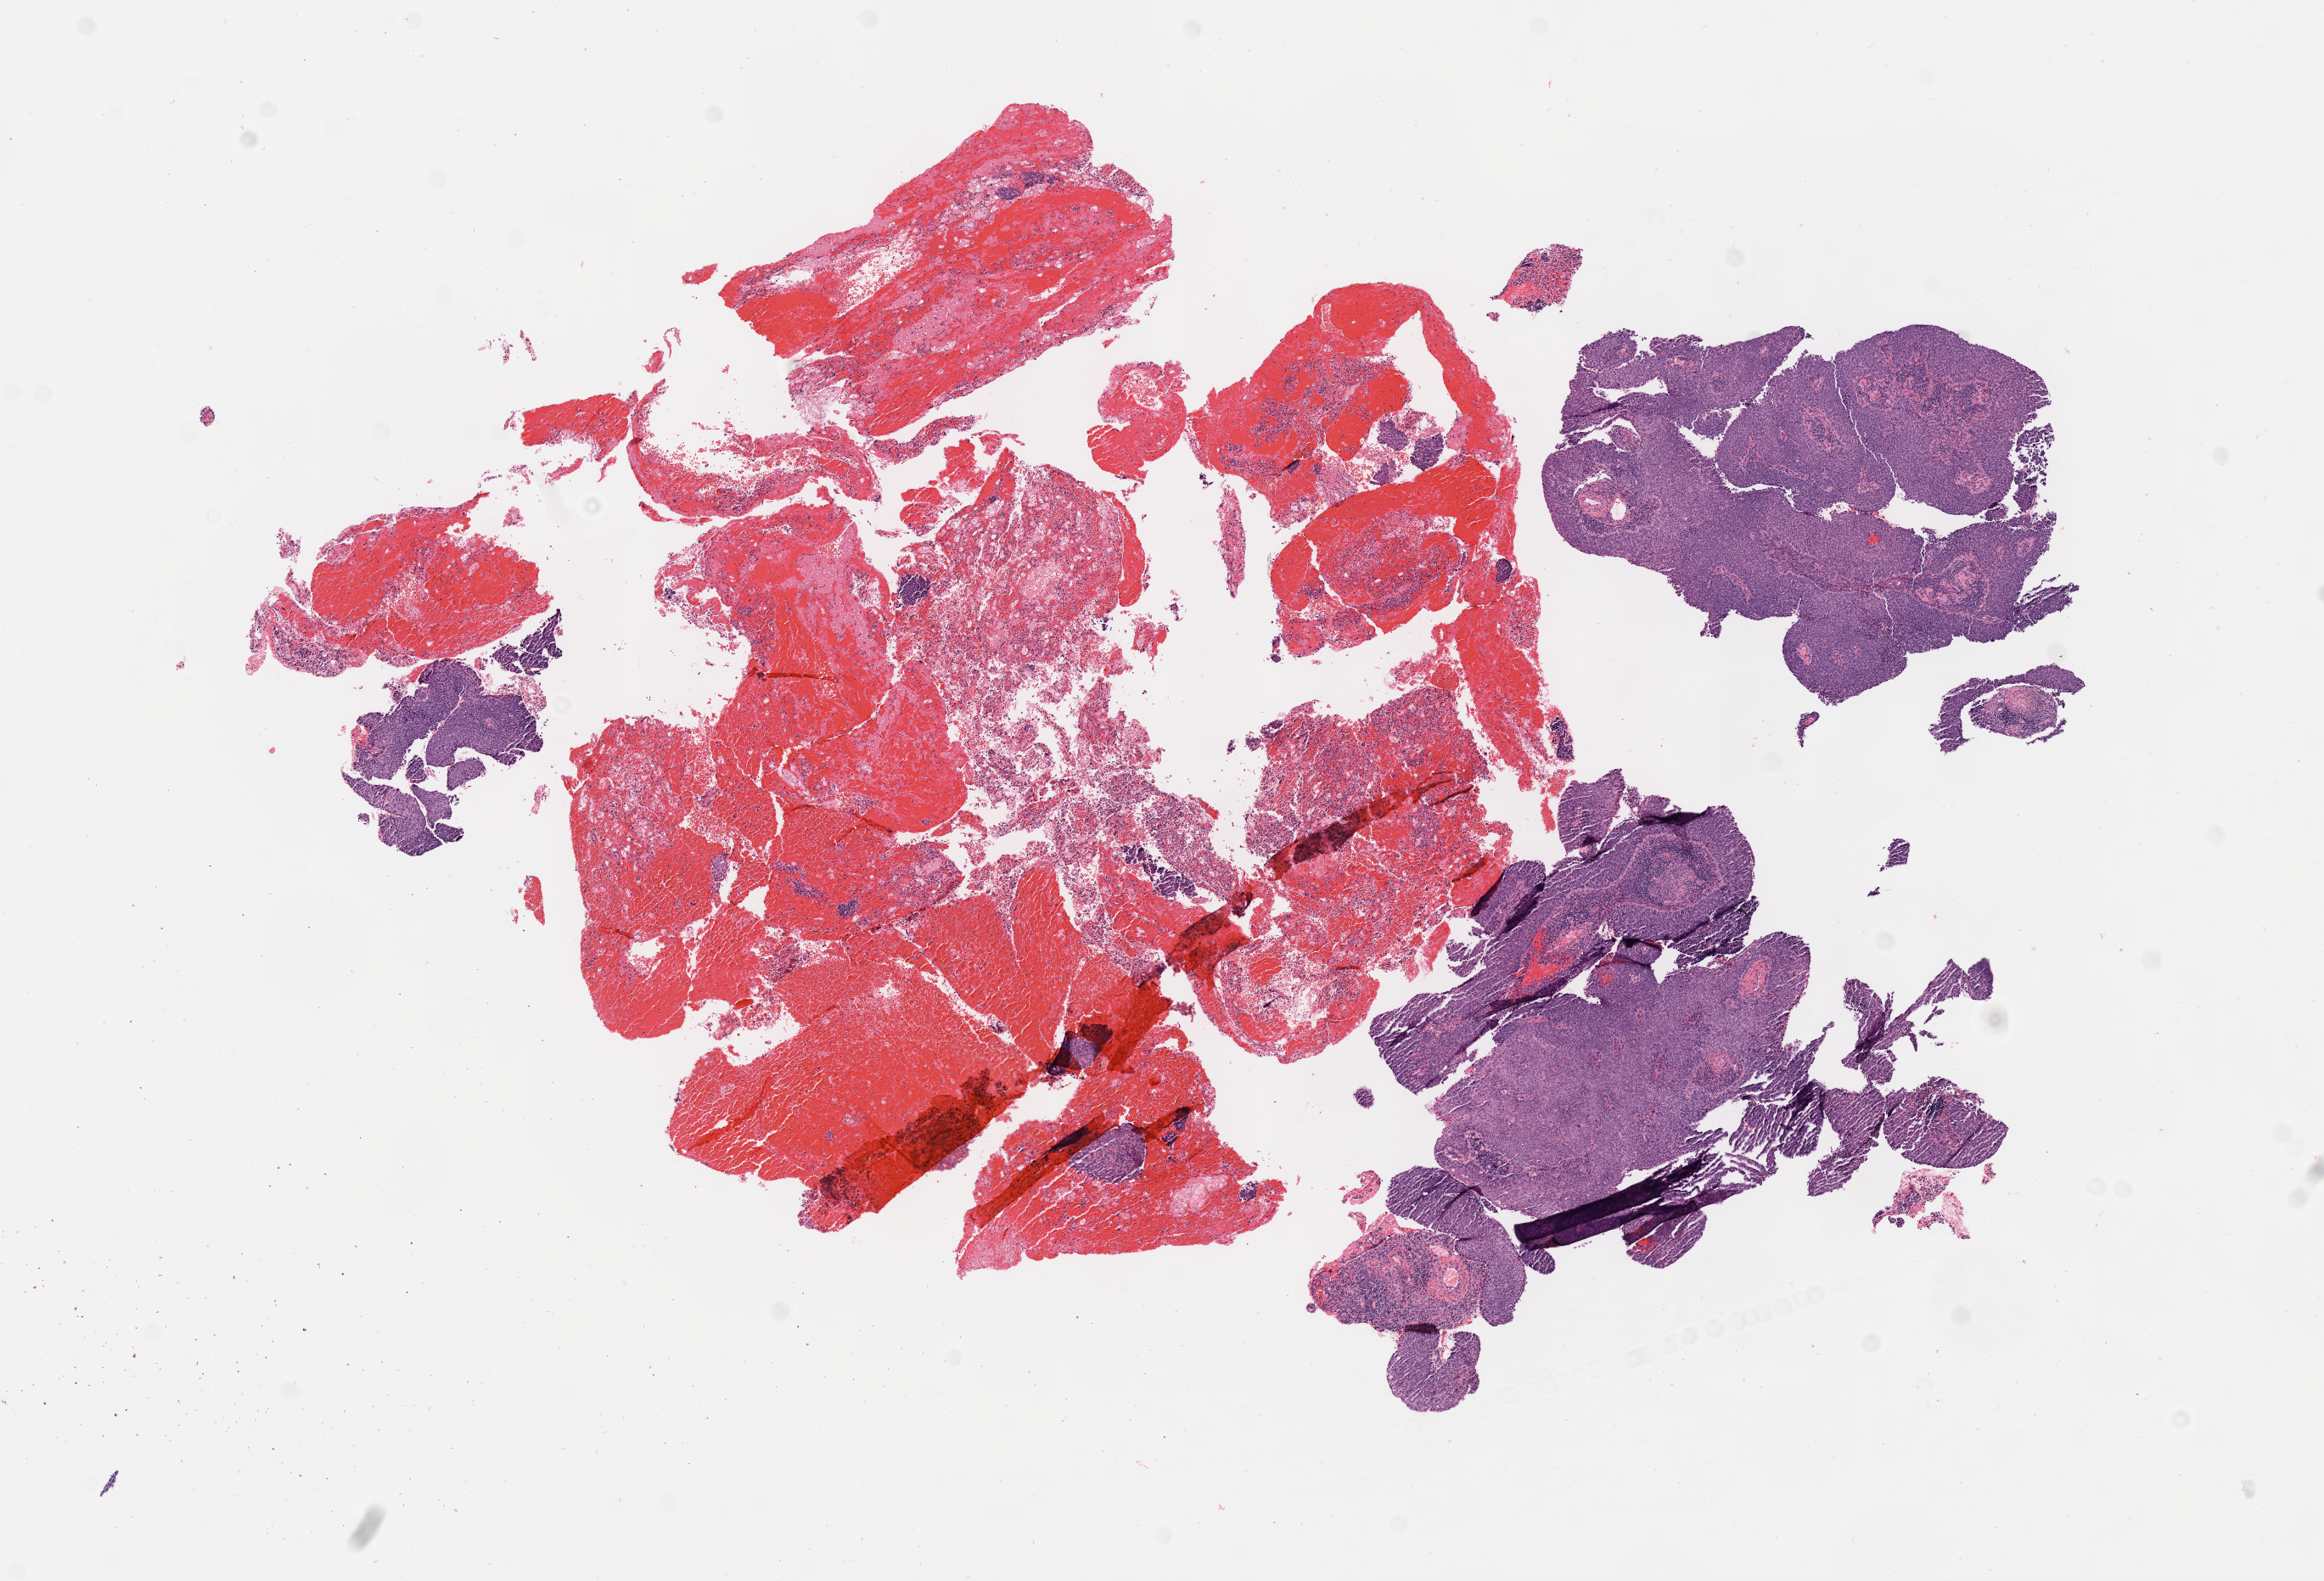
Haematoxylin and eosin whole-slide image — low-resolution overview of the scanned area, about 11.1 x 7.5 mm; specimen: tumor tissue; site: cervix. Female patient, 33 years old.
Histologic diagnosis: Squamous cell carcinoma, large cell, nonkeratinizing, NOS.